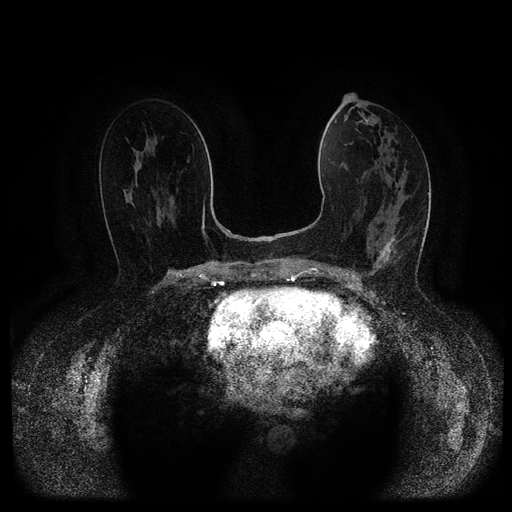
Breast MRI (dynamic contrast-enhanced, multi-phase), one axial slice. Dynamic contrast-enhanced series, time point 2 of 5 at this slice position (early post-contrast). 1.5 T. TE 2.6 ms, TR 5.4 ms. 2 mm slice thickness. 512 × 512 image matrix. Patient: female, 61 years.
Annotated regions visible in this slice (semi-automatically segmented with operator editing):
- breast lesion (labelled 'tumour' in the annotation; benign lesions carry a separate 'benign' label): bounding box [x1, y1, x2, y2] px = [373, 237, 395, 269]